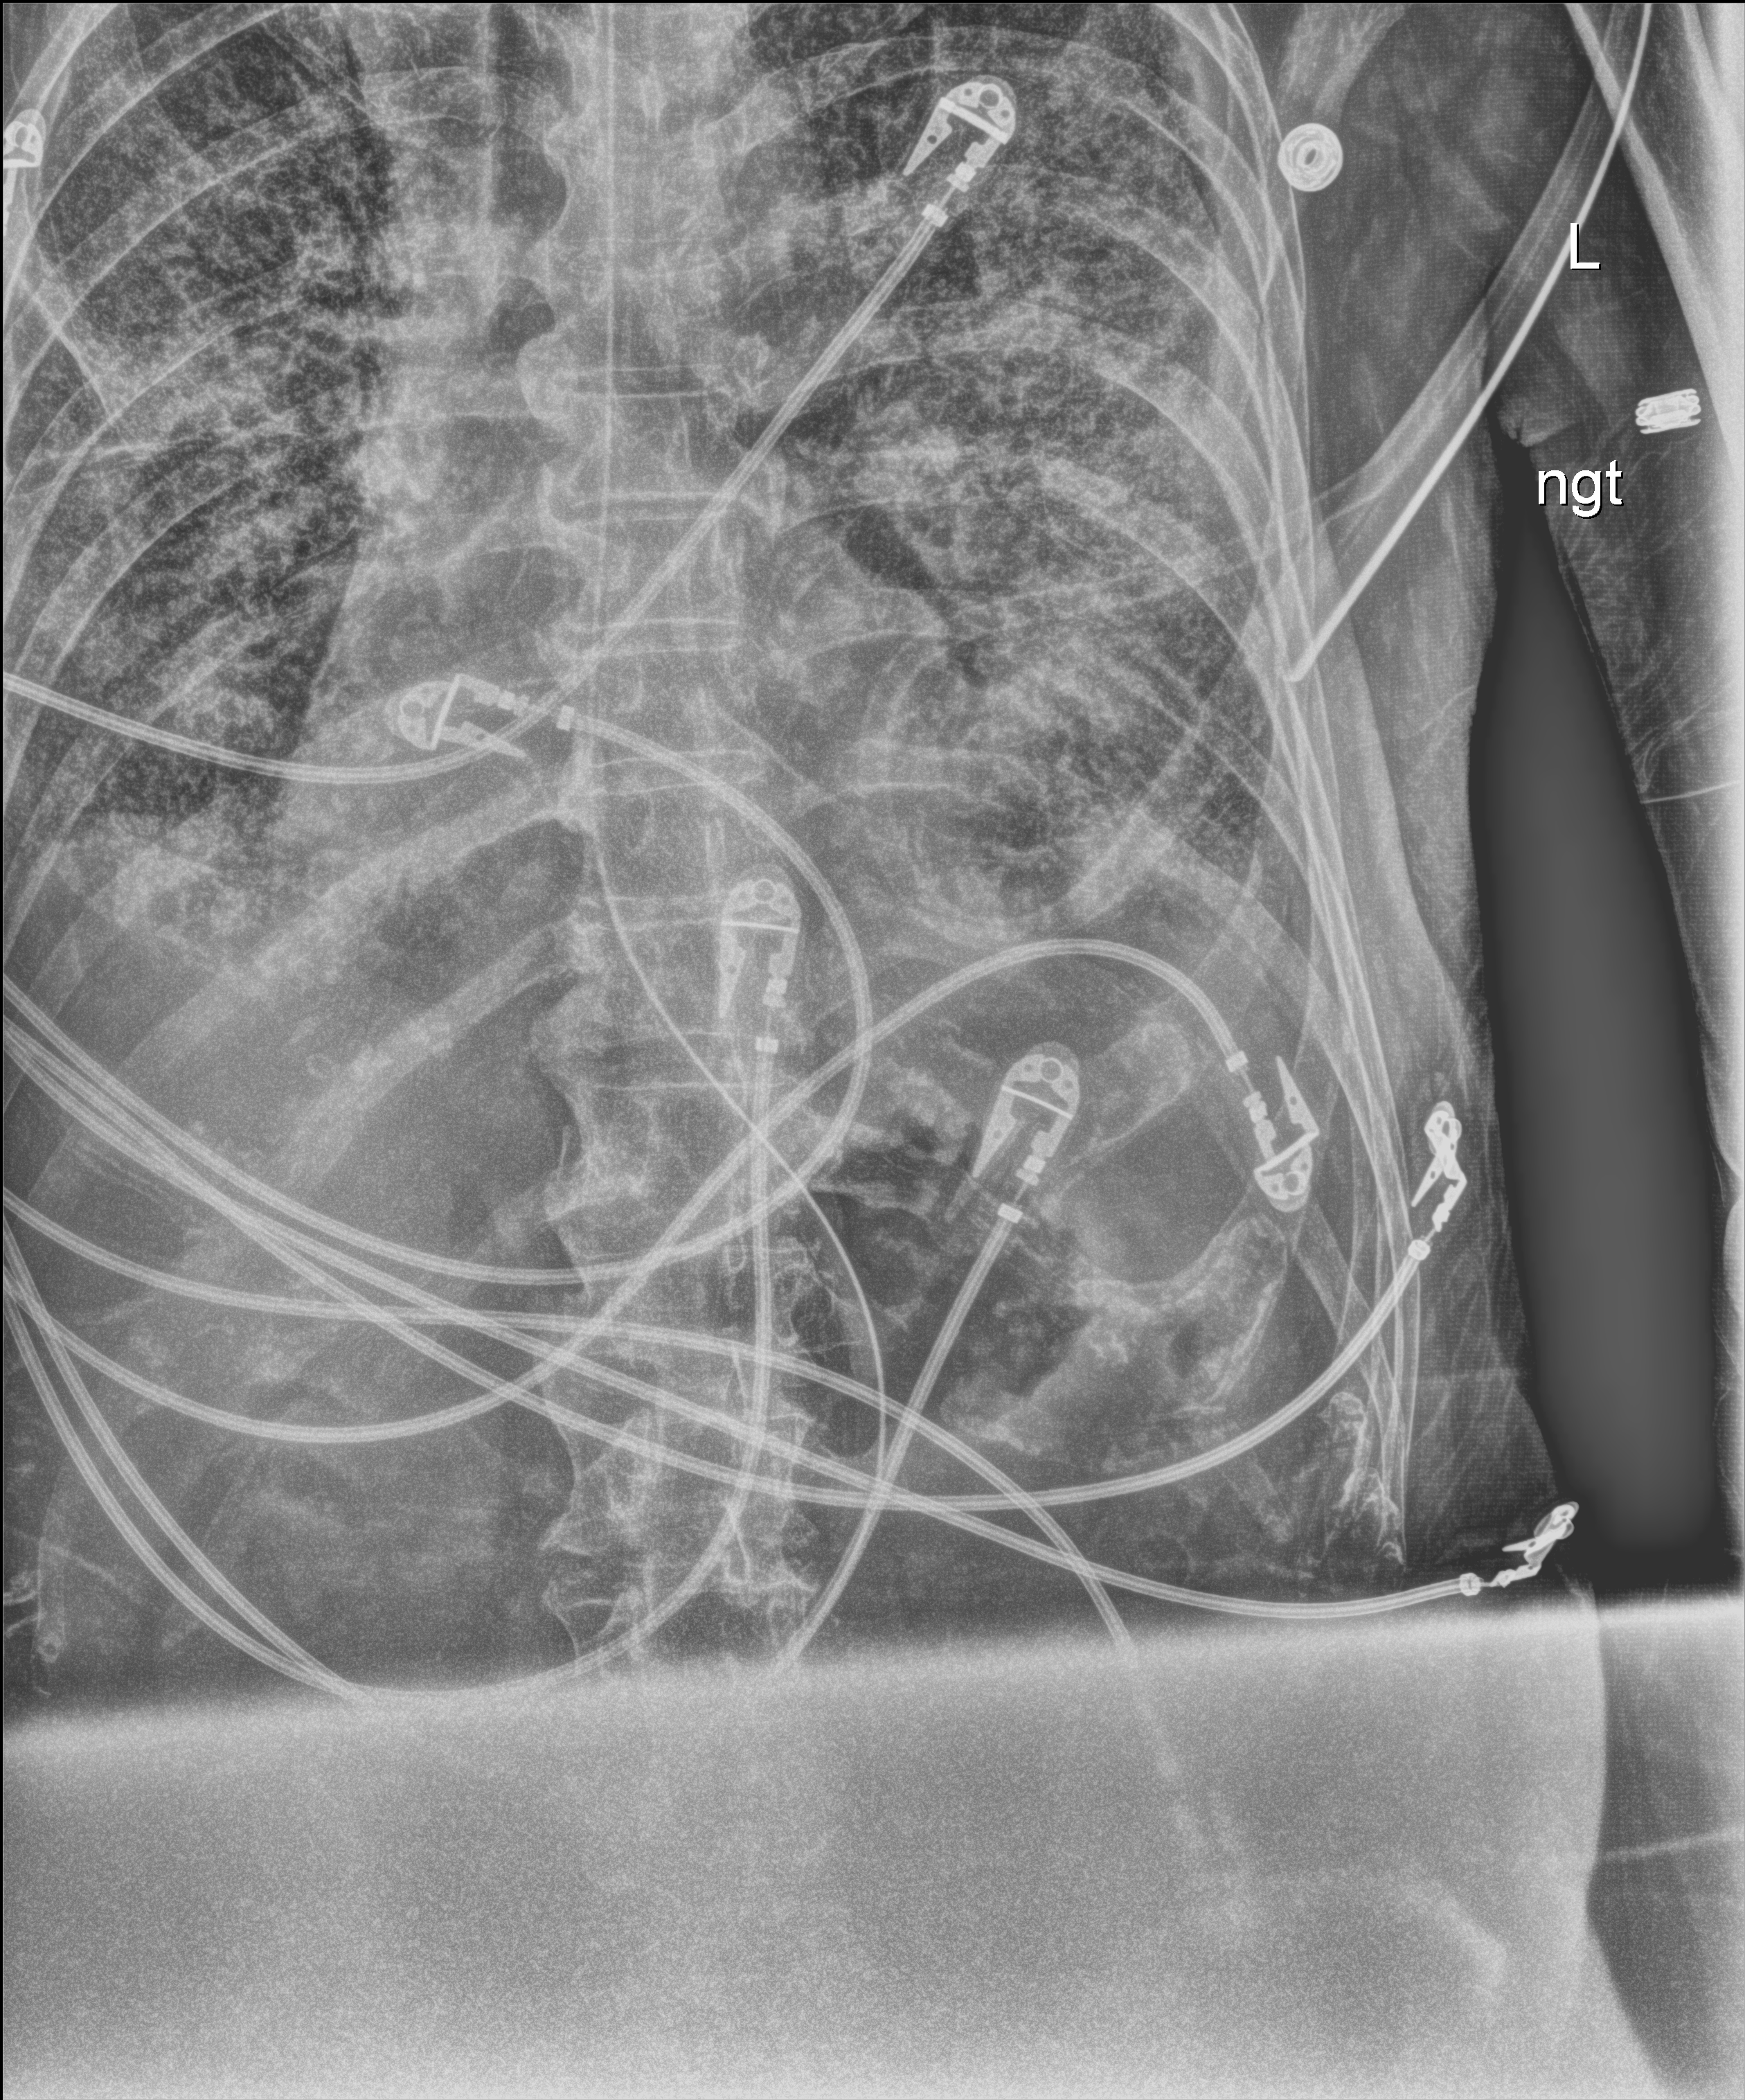
Chest X-ray (portable); anteroposterior (AP) projection. Male patient hospitalised with COVID-19, age 60–74 years.
Hospital-stay facts (about this admission, not read from this image; timing relative to this image not recorded): mechanically ventilated during this hospital stay: yes; admitted to intensive care during this hospital stay: yes.